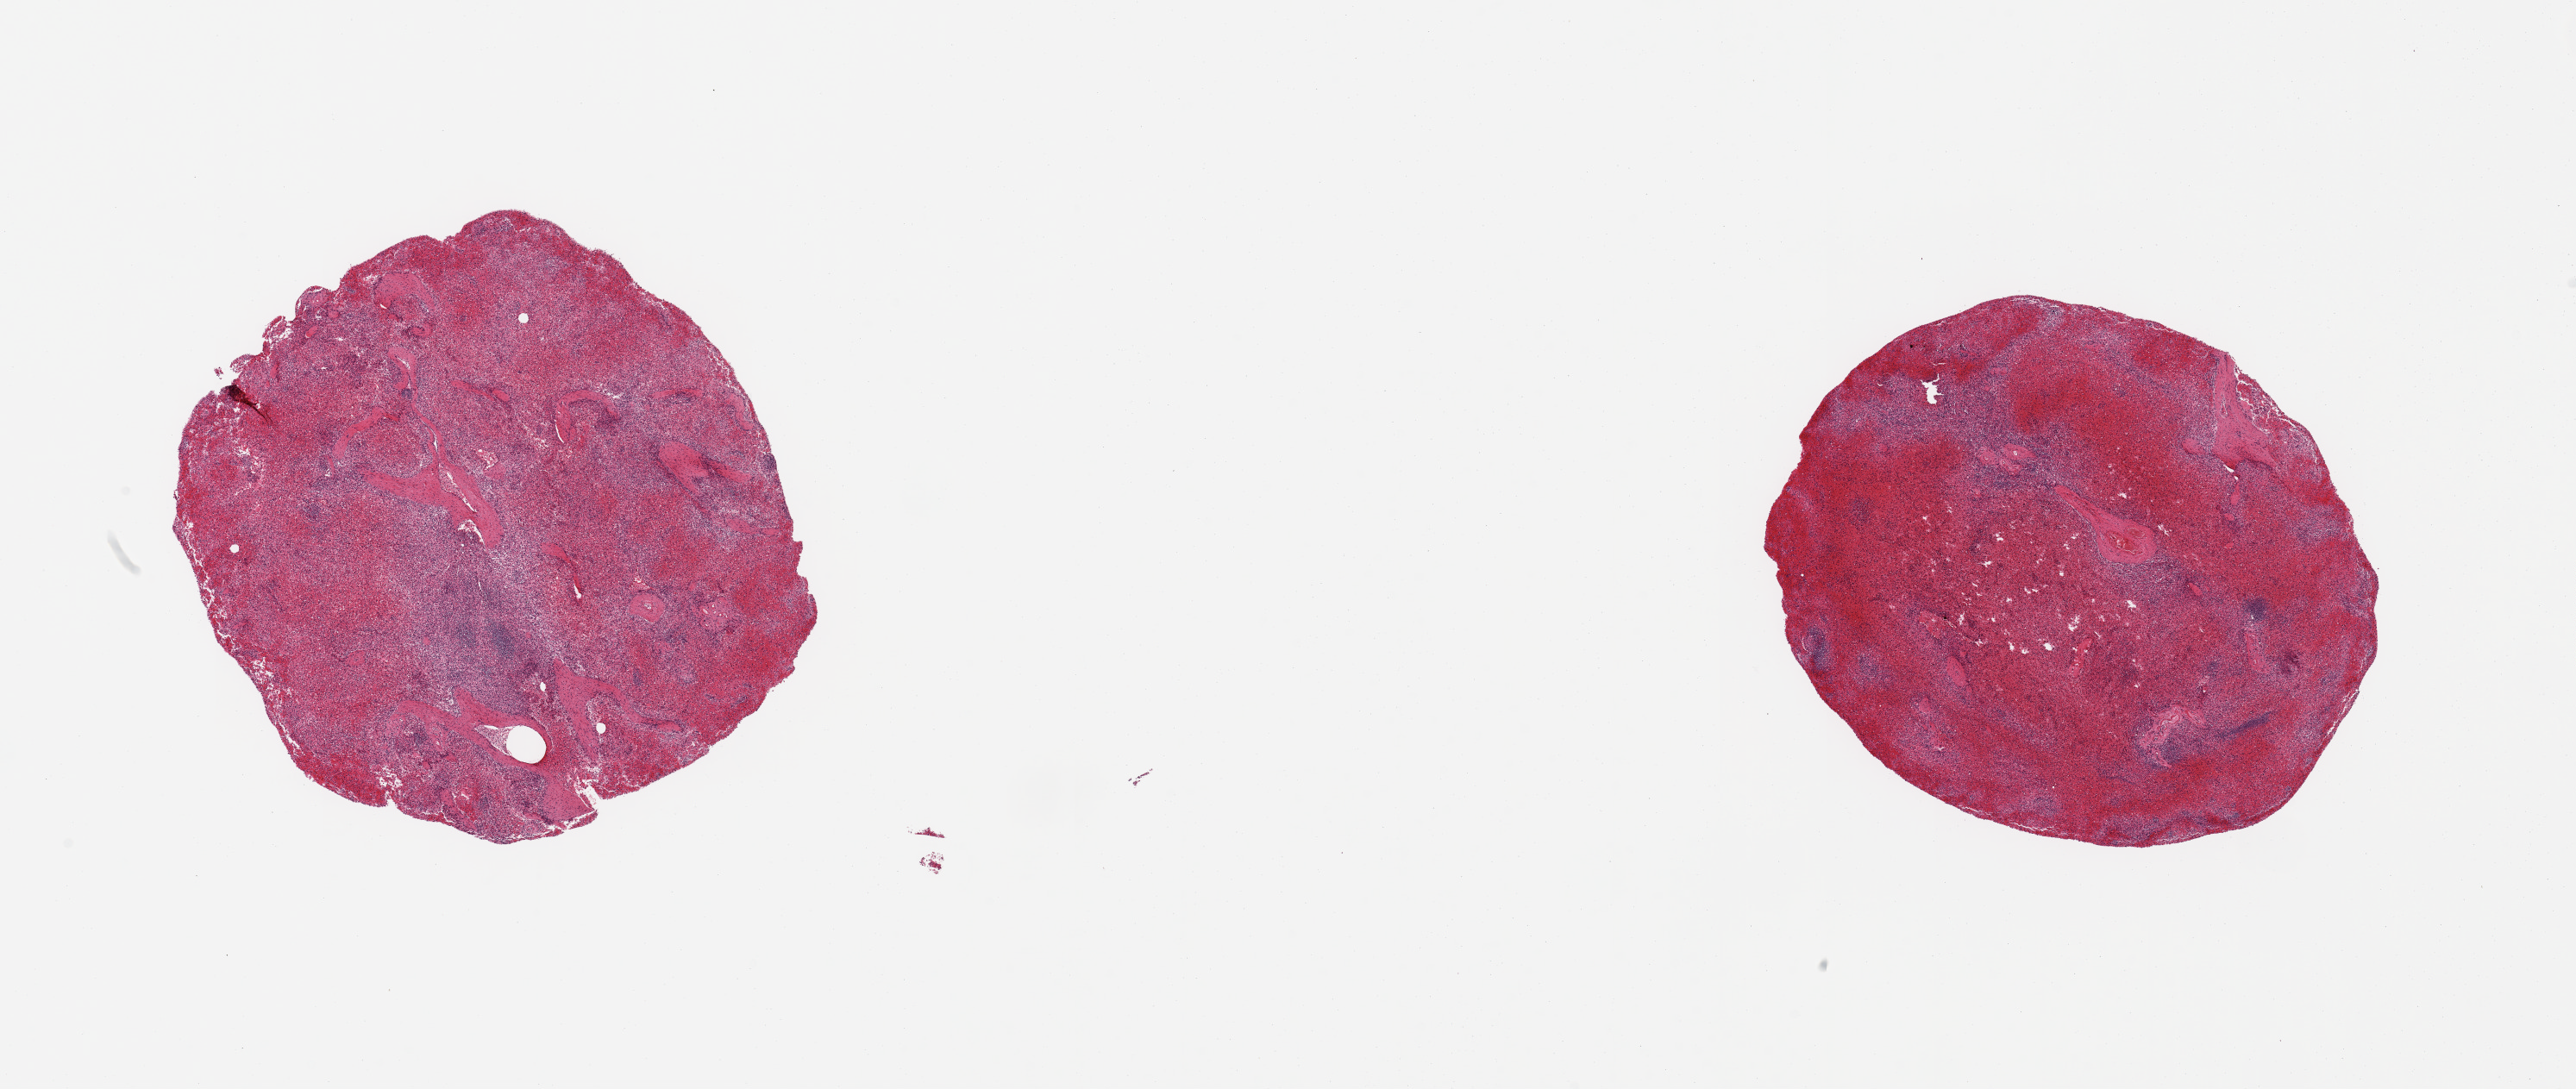
Digitized H&E-stained section, low-resolution overview of the scanned area, about 23.6 x 10.0 mm, PAXgene-fixed paraffin-embedded (PFPE) section, sampled site (target tissue): spleen, donor tissue sample. Donor sex: male.
- reviewer comment on this tissue sample: 2 pieces; moderate congestion